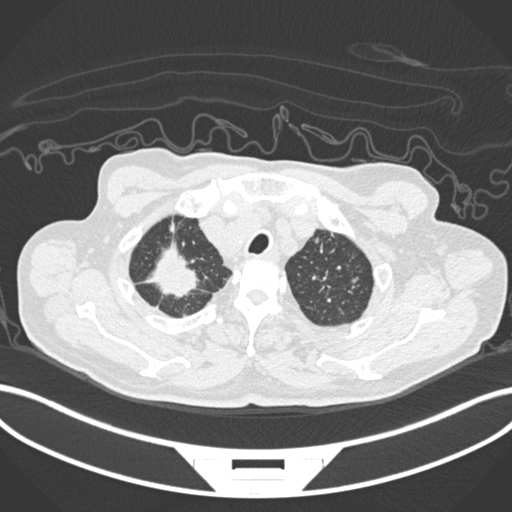
Chest CT, one axial slice; position 191 of 207 along the scan axis; lung window (W 1500 / L -600 HU); 512 × 512 image matrix, field of view 400 × 400 mm. Patient: male, 69 years. From the clinical record (not read from this slice): clinical TNM (as recorded): T1c N1 M1.
Structures marked on this image (bounding box drawn by a radiologist):
- lung tumour (recorded histology: adenocarcinoma): box from (x=146, y=243) to (x=202, y=304) px